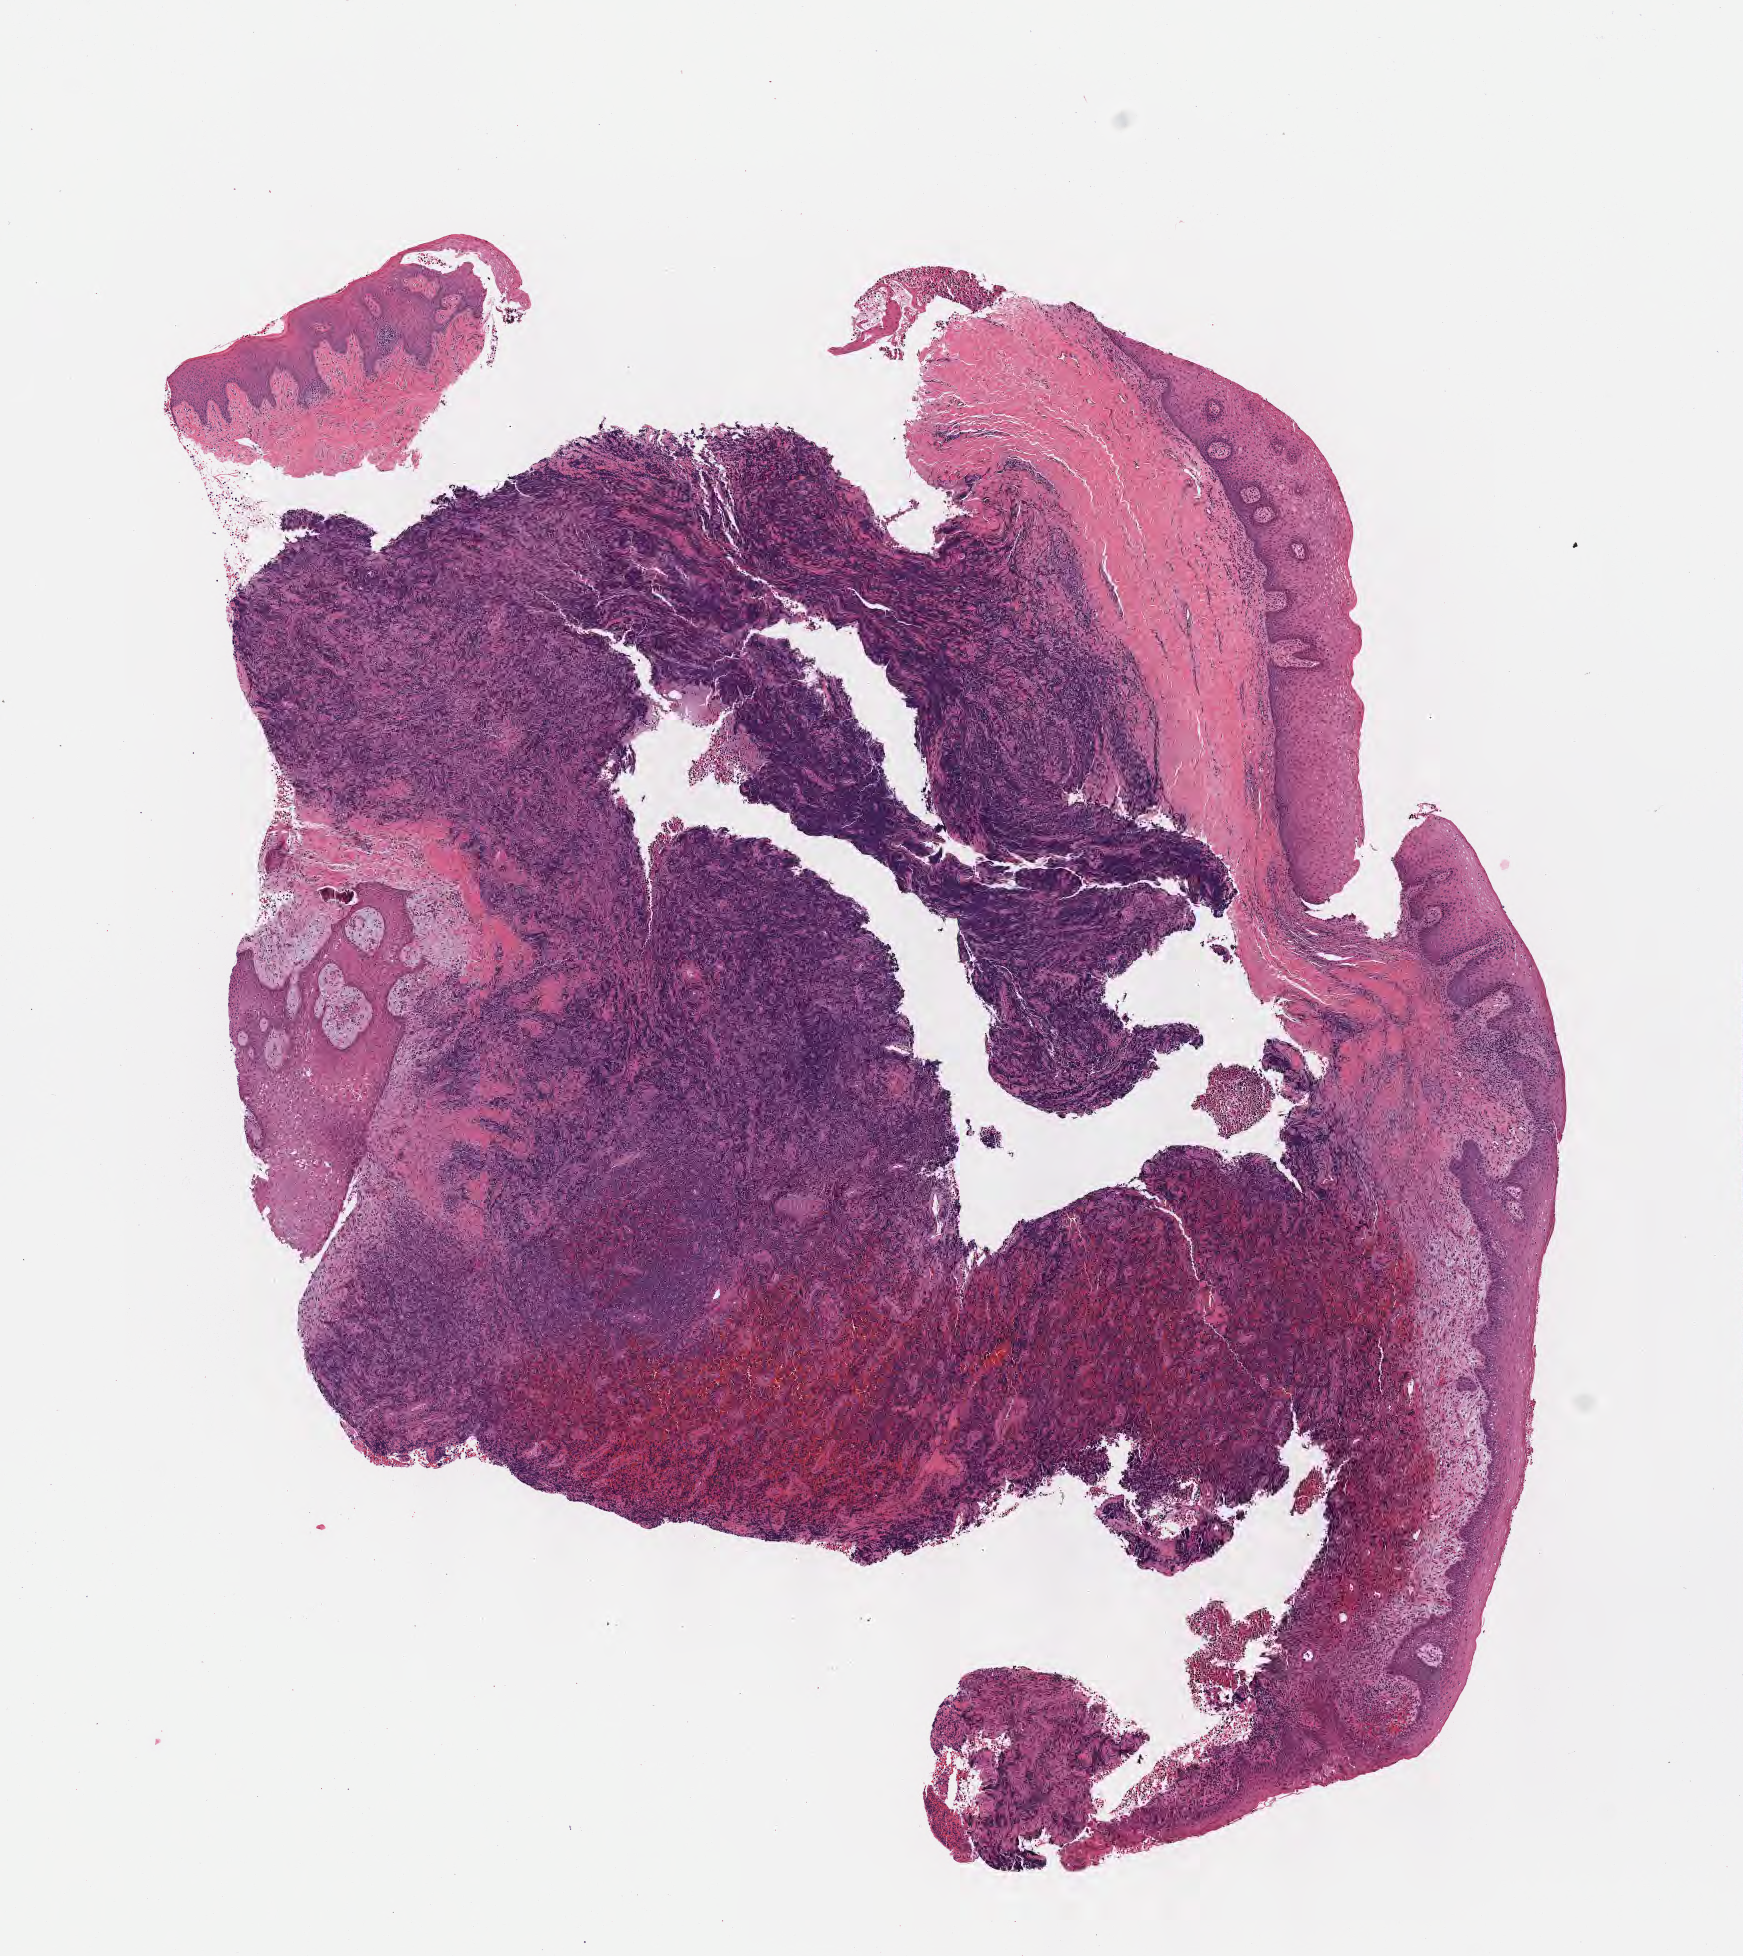
Whole-slide image, H&E stain — a low-resolution overview of the entire scanned area, about 7.0 x 7.9 mm. Specimen: tumor tissue. Site: mandible. Patient: female, age at initial diagnosis 7 years.
Histologic diagnosis: Burkitt lymphoma, NOS.